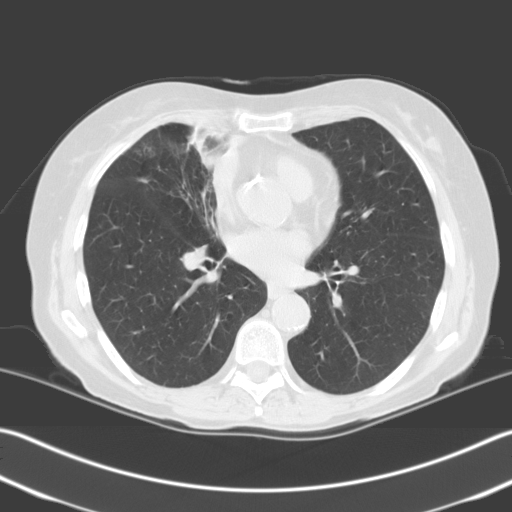
Low-dose screening chest CT, one axial slice. Slice 109 of 204 in the series (ordered by position). 140 kVp. Lung window (W 1500 / L -600 HU). 3.2 mm slice thickness. 512 × 512 image matrix.
Annotated regions visible in this slice (manually delineated by an expert):
- lesion 1 (tumor, upper lobe of right lung): bounding box [x1, y1, x2, y2] px = [189, 131, 244, 172]